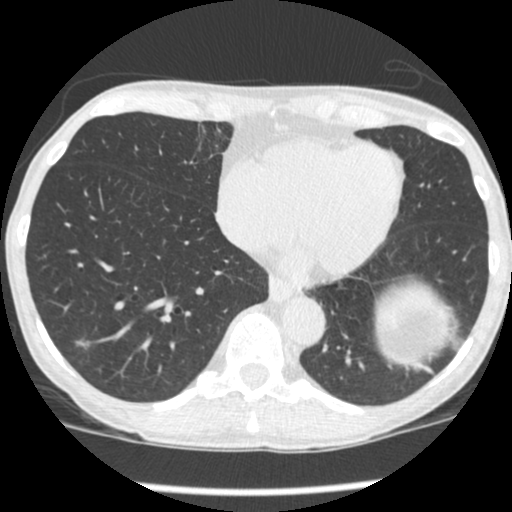
Low-dose screening chest CT, one axial slice. Slice 85 of 248 in the series (ordered by position). Reconstruction kernel STANDARD. Lung window (W 1500 / L -600 HU). 1.25 mm slice thickness. 512 × 512 image matrix, field of view 293 × 293 mm.
Structures marked on this image (expert manual segmentation):
- lesion 1 (tumor, lower lobe of right lung): bounding box <76,341,90,348> (left, top, right, bottom; pixels)